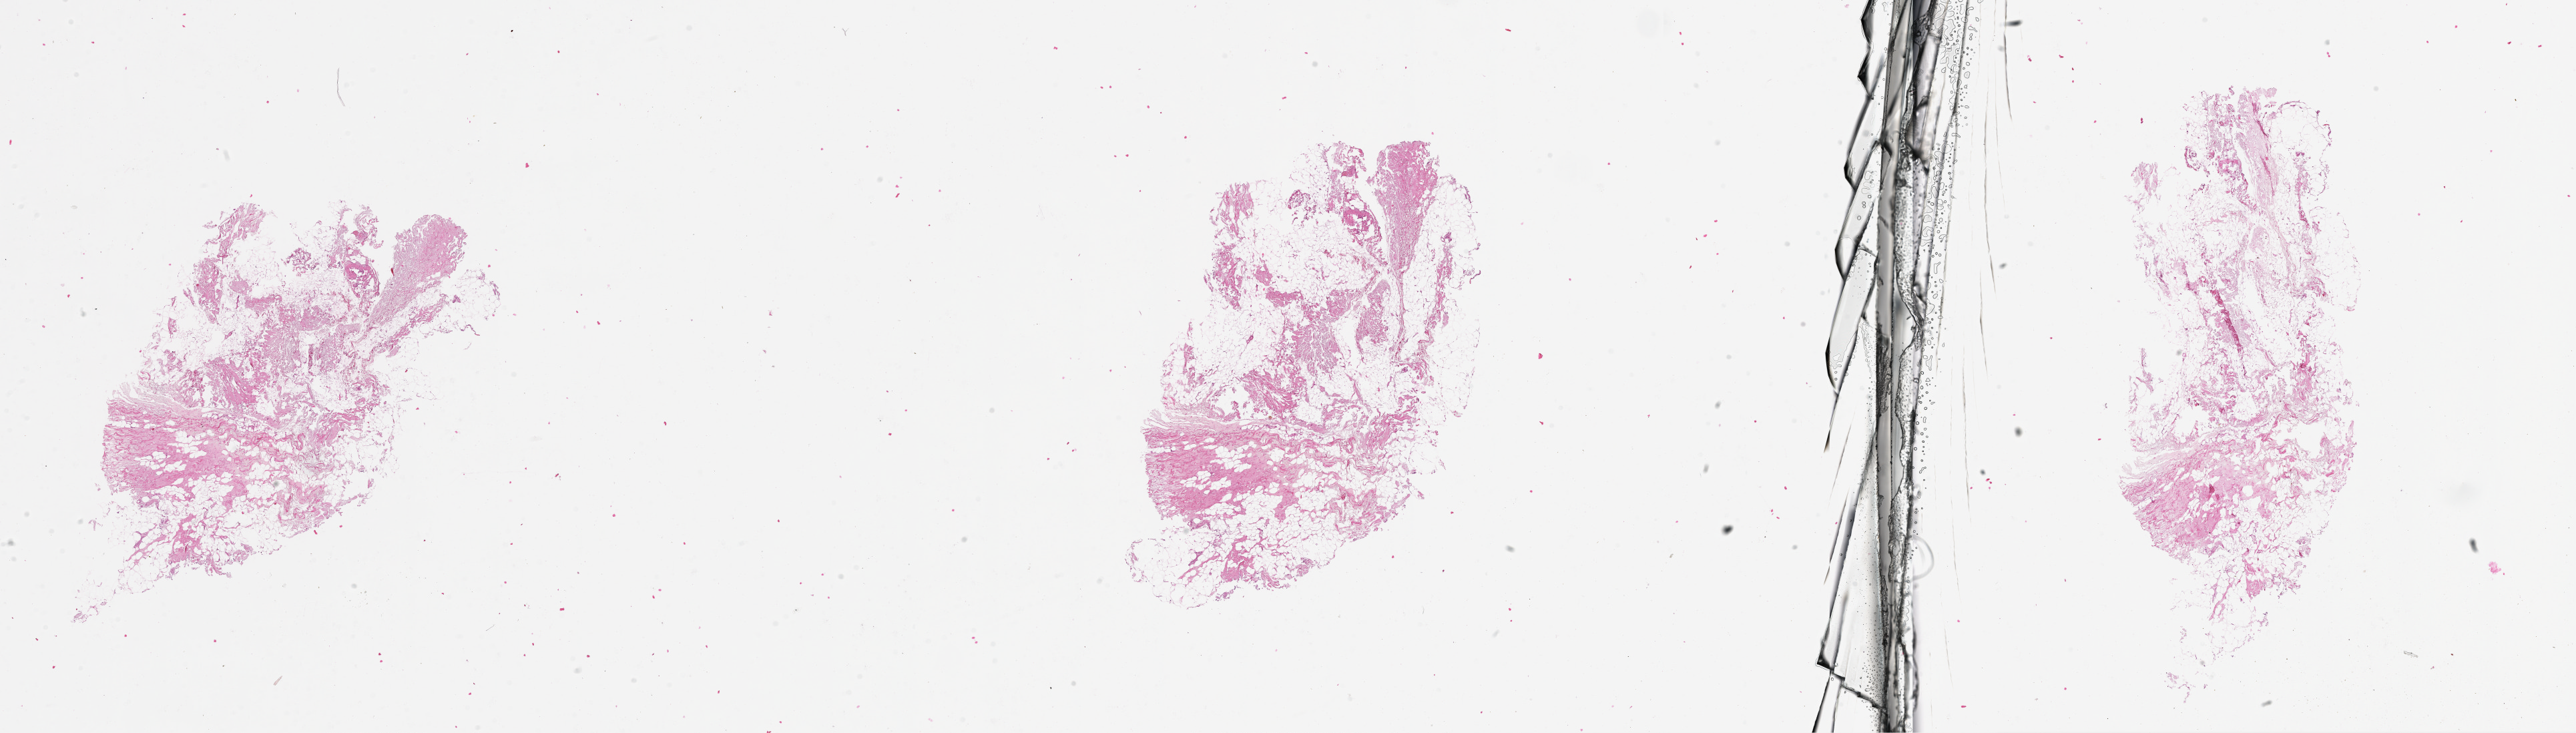
Digitized H&E tissue section (whole slide) — low-resolution overview of the scanned area, about 31.1 x 8.8 mm. Patient: male, age 72 years.
Patient diagnosis: Malignant melanoma, NOS.